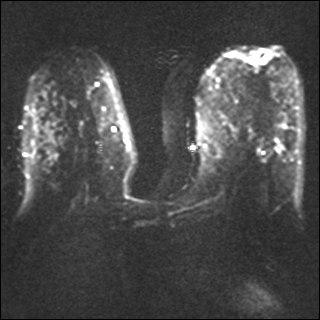
Breast MRI, one axial slice; slice 18 of 40 in the series (ordered by position); diffusion-weighted series; image 2 of 4 stored at this slice position (different b-values; order by instance number); 1.5 T; 320 × 320 image matrix, field of view 330 × 330 mm. Female patient.
Structures marked on this image (manually delineated by an expert):
- tumour on diffusion-weighted imaging: box from (x=251, y=52) to (x=260, y=62) px